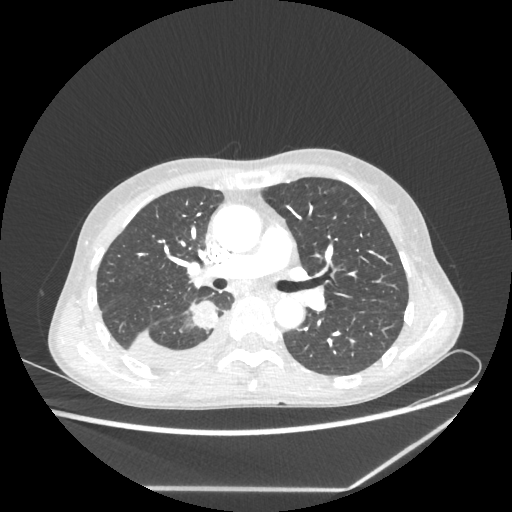
Chest CT, one axial slice. Slice 138 of 237 in the series (ordered by position). Lung window (W 1500 / L -600 HU). 1.25 mm slice thickness. 512 × 512 image matrix, field of view 364 × 364 mm. Female patient, age 59 years. Case-level facts recorded for this patient, not image findings: clinical TNM (as recorded): T1c N1 M1.
Annotated regions visible in this slice (rectangle marked by the reading radiologist):
- lung tumour (recorded histology: adenocarcinoma): bounding box (x1, y1, x2, y2) in pixels: (188, 299, 220, 330)